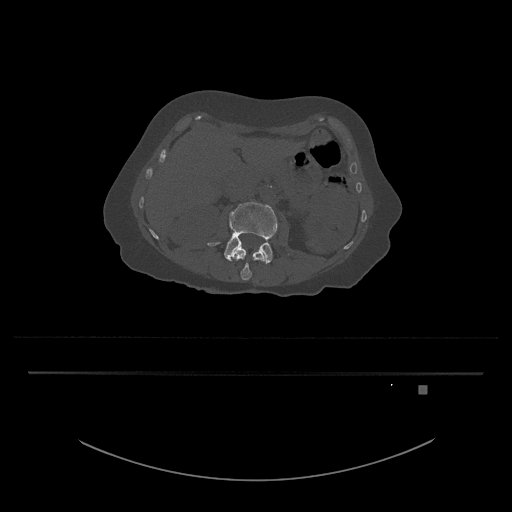
CT including the spine, one axial slice; bone window (W 1800 / L 400 HU); 0.5 mm slice thickness; 512 × 512 image matrix, field of view 500 × 500 mm. Patient: female, 57 years. Case-level facts recorded for this patient, not image findings: primary cancer: cervical.
Annotated regions visible in this slice (semi-automatically segmented with operator editing):
- L3 vertebra: bounding box <207,201,278,264> (left, top, right, bottom; pixels)